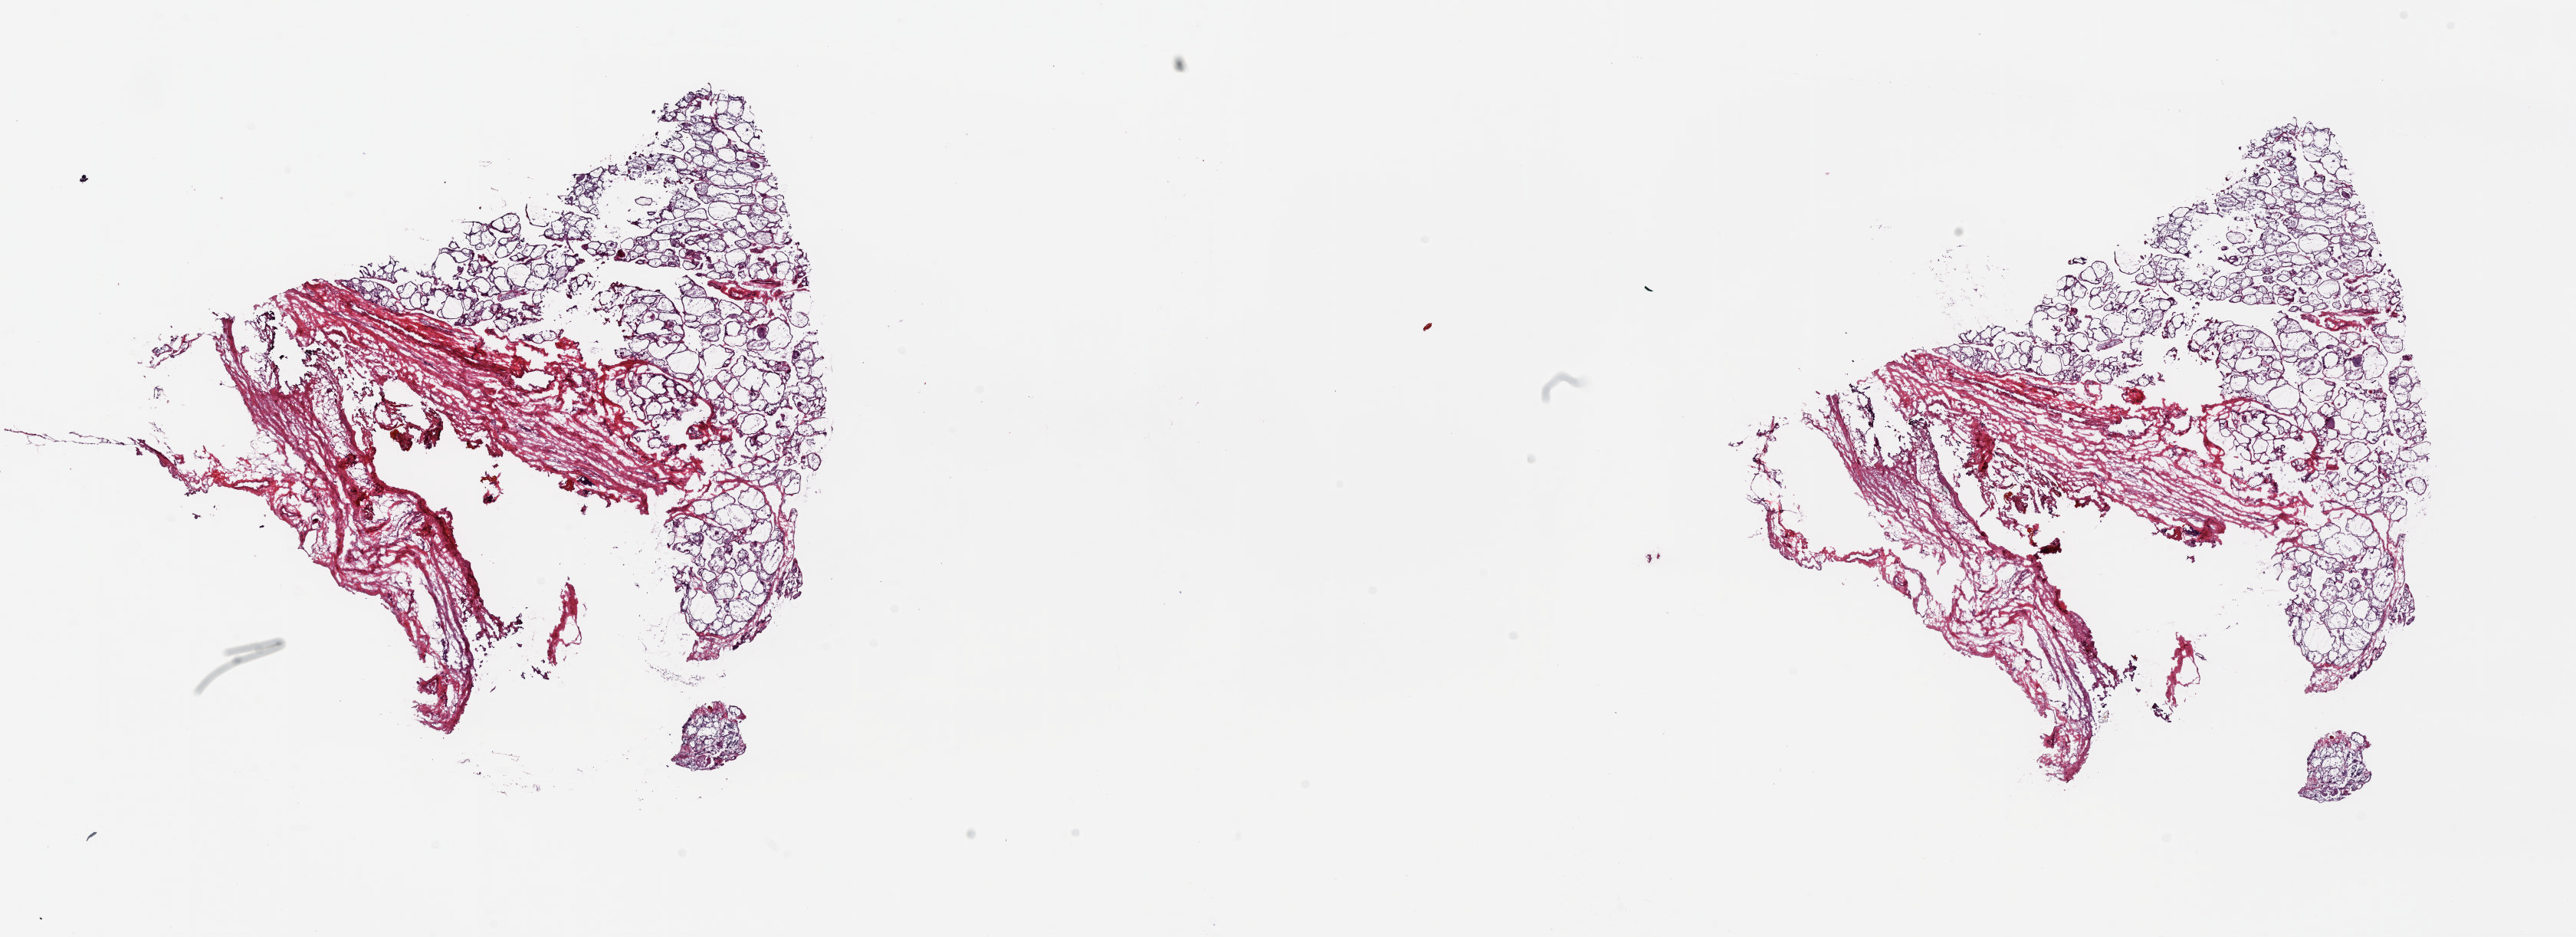
Digitized H&E tissue section (whole slide), shown as a low-resolution overview of the whole scanned area (about 26.6 x 9.7 mm). Frozen section from the top of the tissue portion. Solid tissue normal (non-tumour tissue) sample from the thyroid. Female patient; age at initial diagnosis 55 years. Composition of this section per pathologist review: tumour cells 0%, tumour nuclei 0%, normal cells 100%, stromal cells 0%, necrosis 0%. Inflammatory infiltration, as recorded: lymphocyte infiltration 0%, monocyte infiltration 4%, neutrophil infiltration 0%.
* this section: solid tissue normal sample (biorepository sample class)
* patient diagnosis: Papillary adenocarcinoma, NOS (thyroid gland)